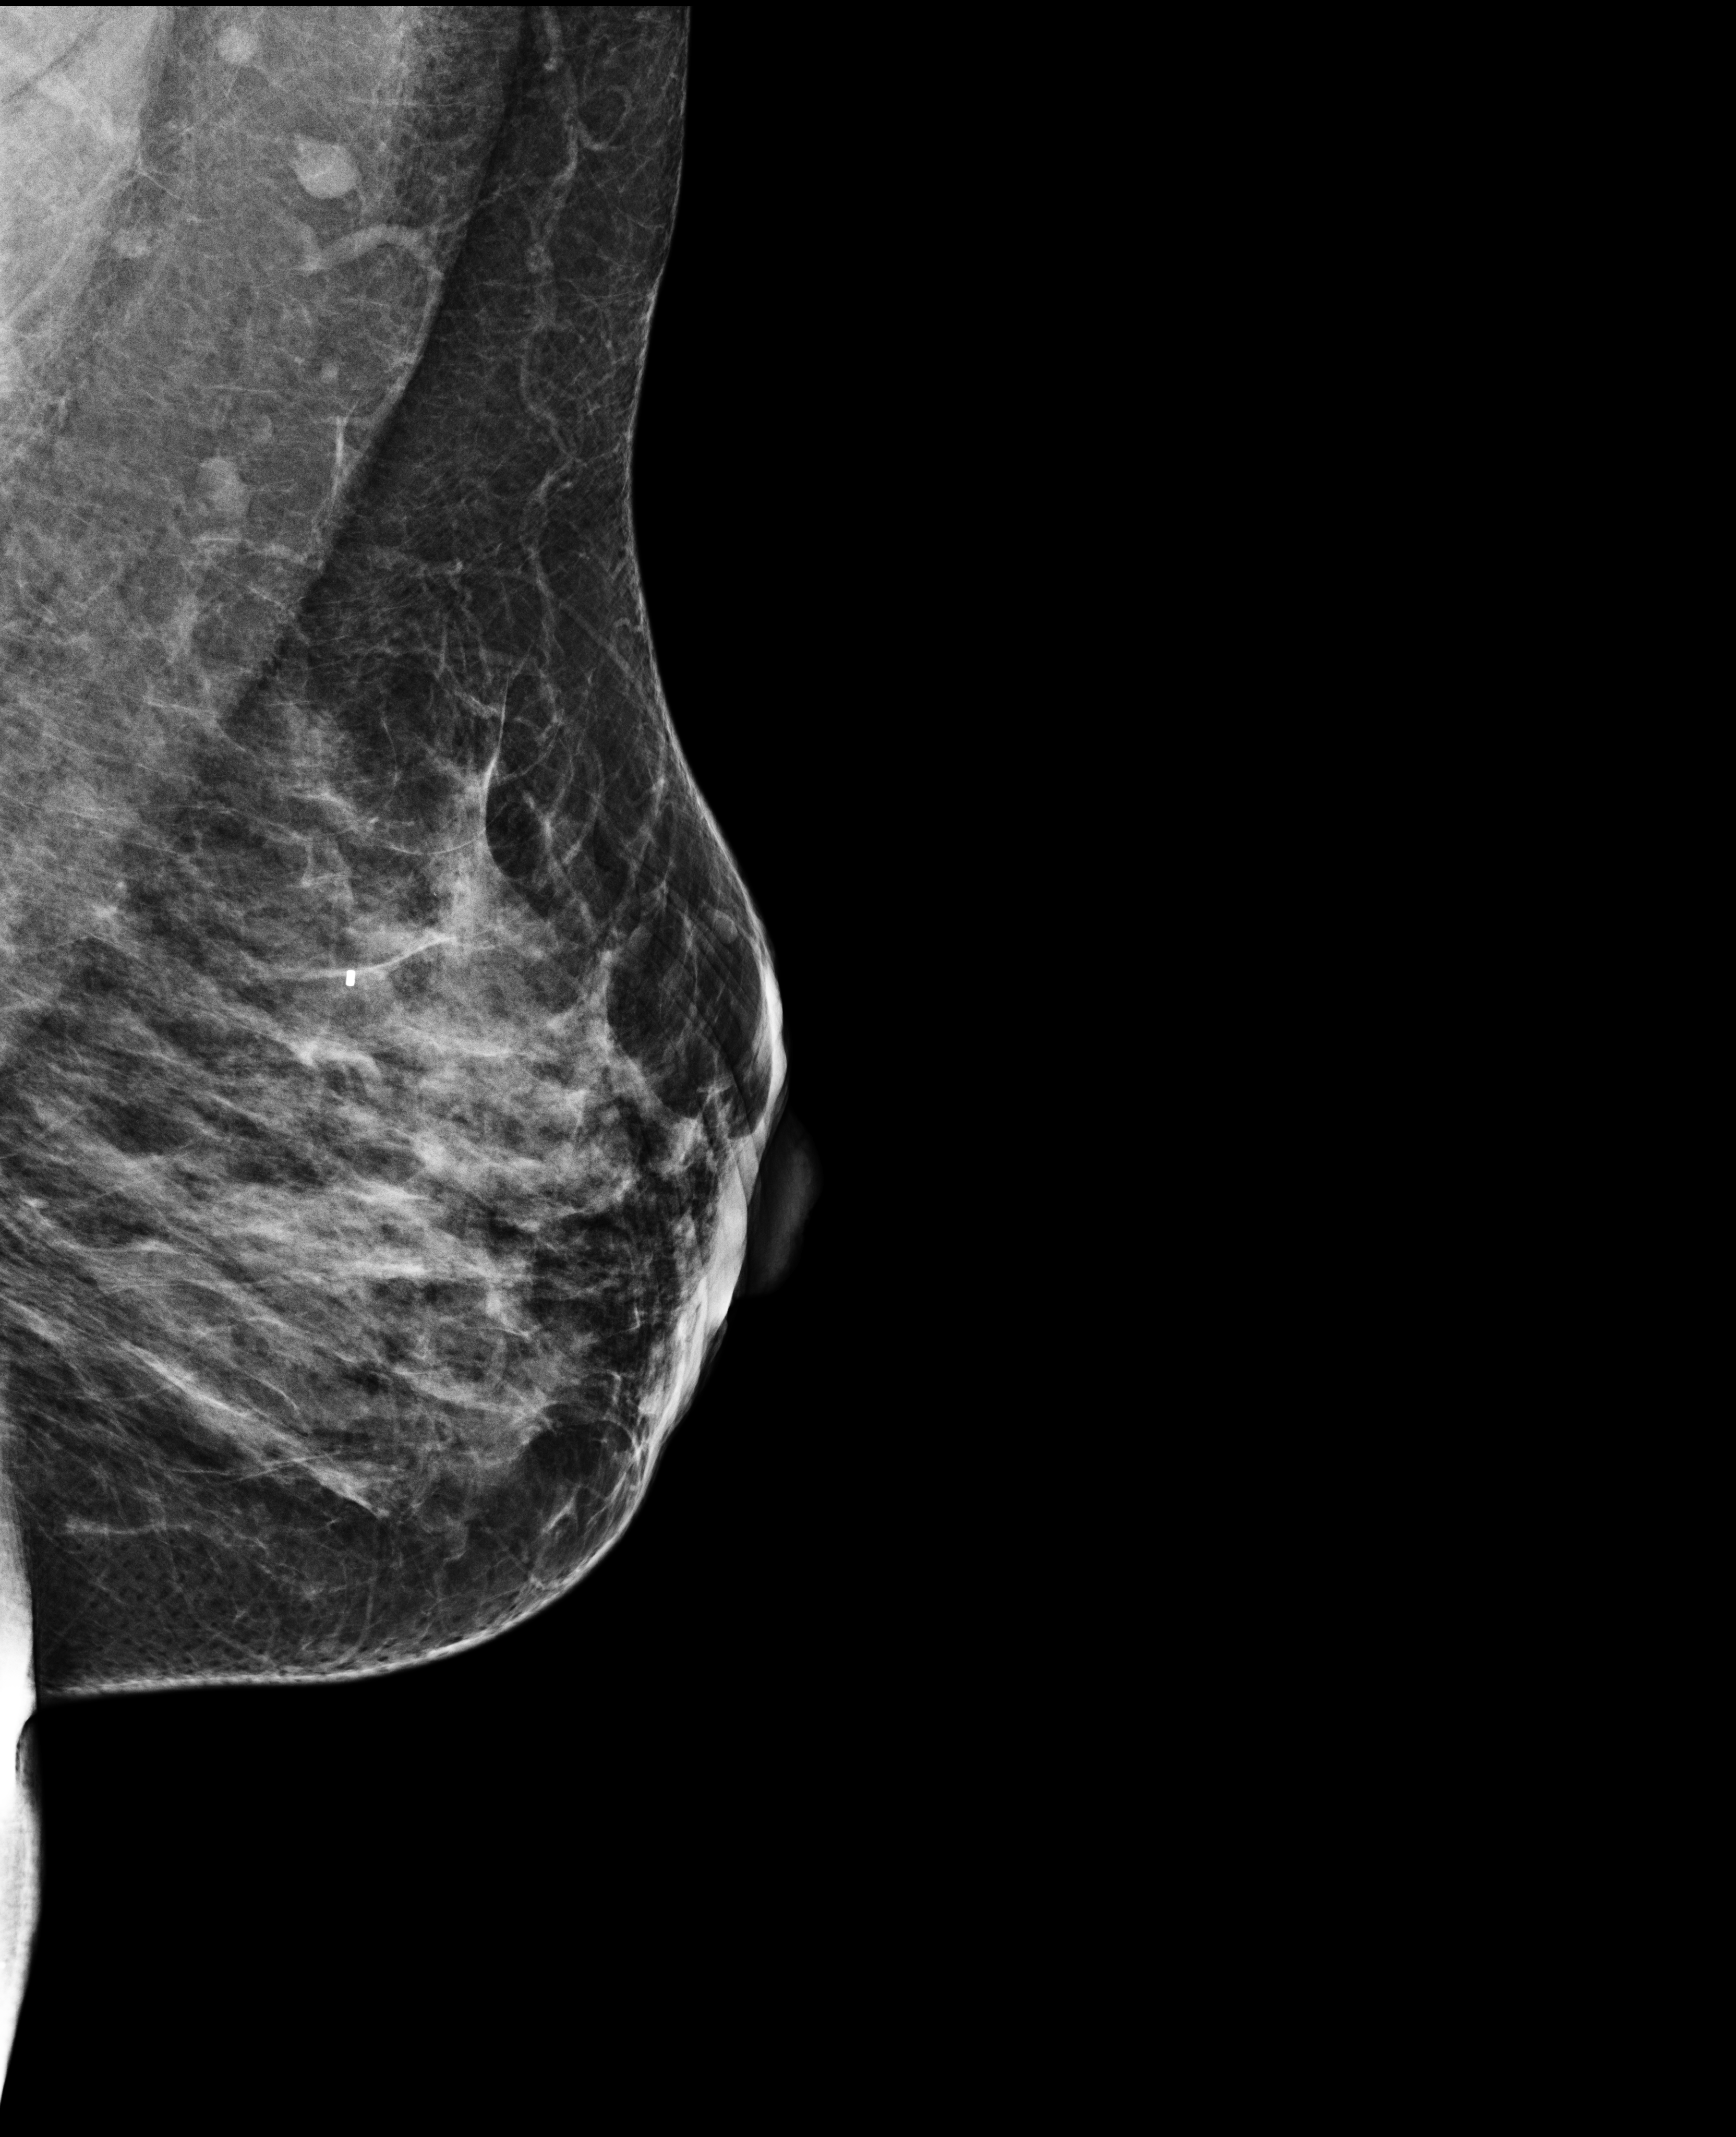
Screening examination, compressed breast thickness 60 mm. Patient aged 43 years (female).
Image type: full-field digital mammogram. Breast: left. Projection: mediolateral oblique (MLO) view.